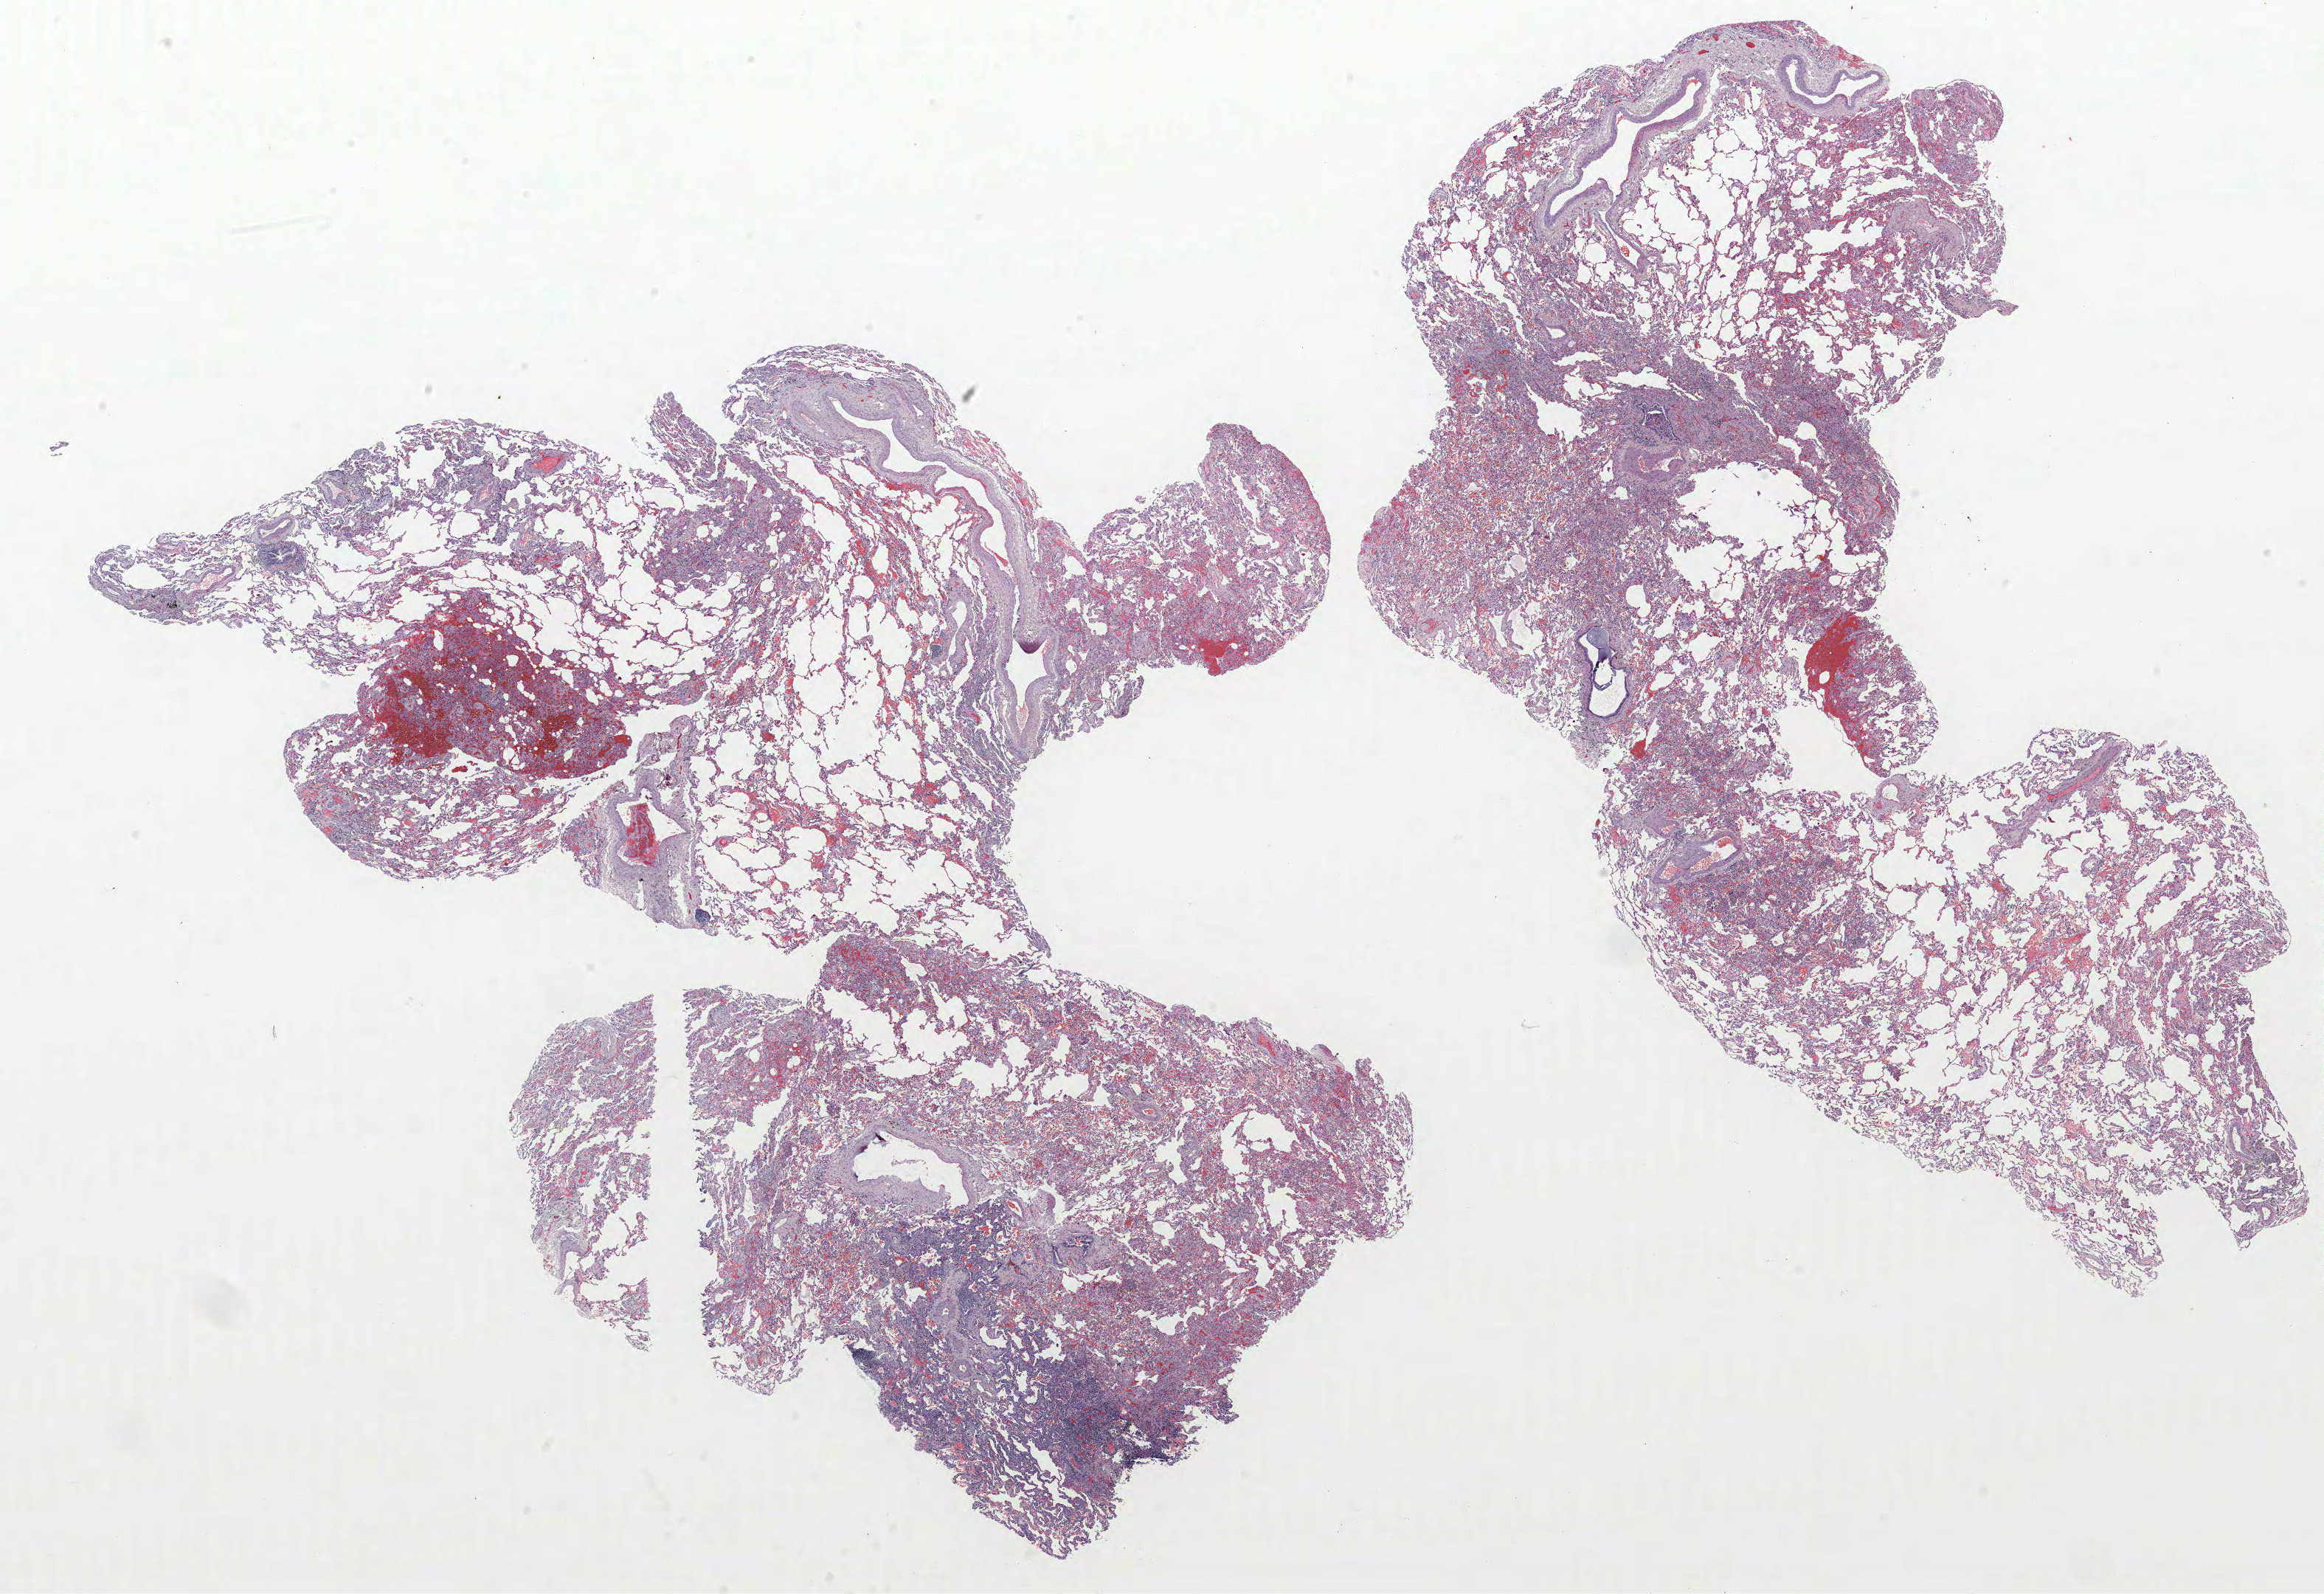
H&E whole-slide image, whole scanned area (about 25.2 x 17.3 mm, slide scanned at 40x) shown as a low-resolution overview, formalin-fixed paraffin-embedded (FFPE) section, lung tissue. Female, age 57 at enrolment. Grade: well differentiated (G1).
Primary tumour location (clinical record): left lower lobe. Stage (AJCC 6th edition): IA. Tumour size (pathology): 16 mm. Participant's lung-cancer diagnosis: Bronchiolo-alveolar adenocarcinoma, NOS.